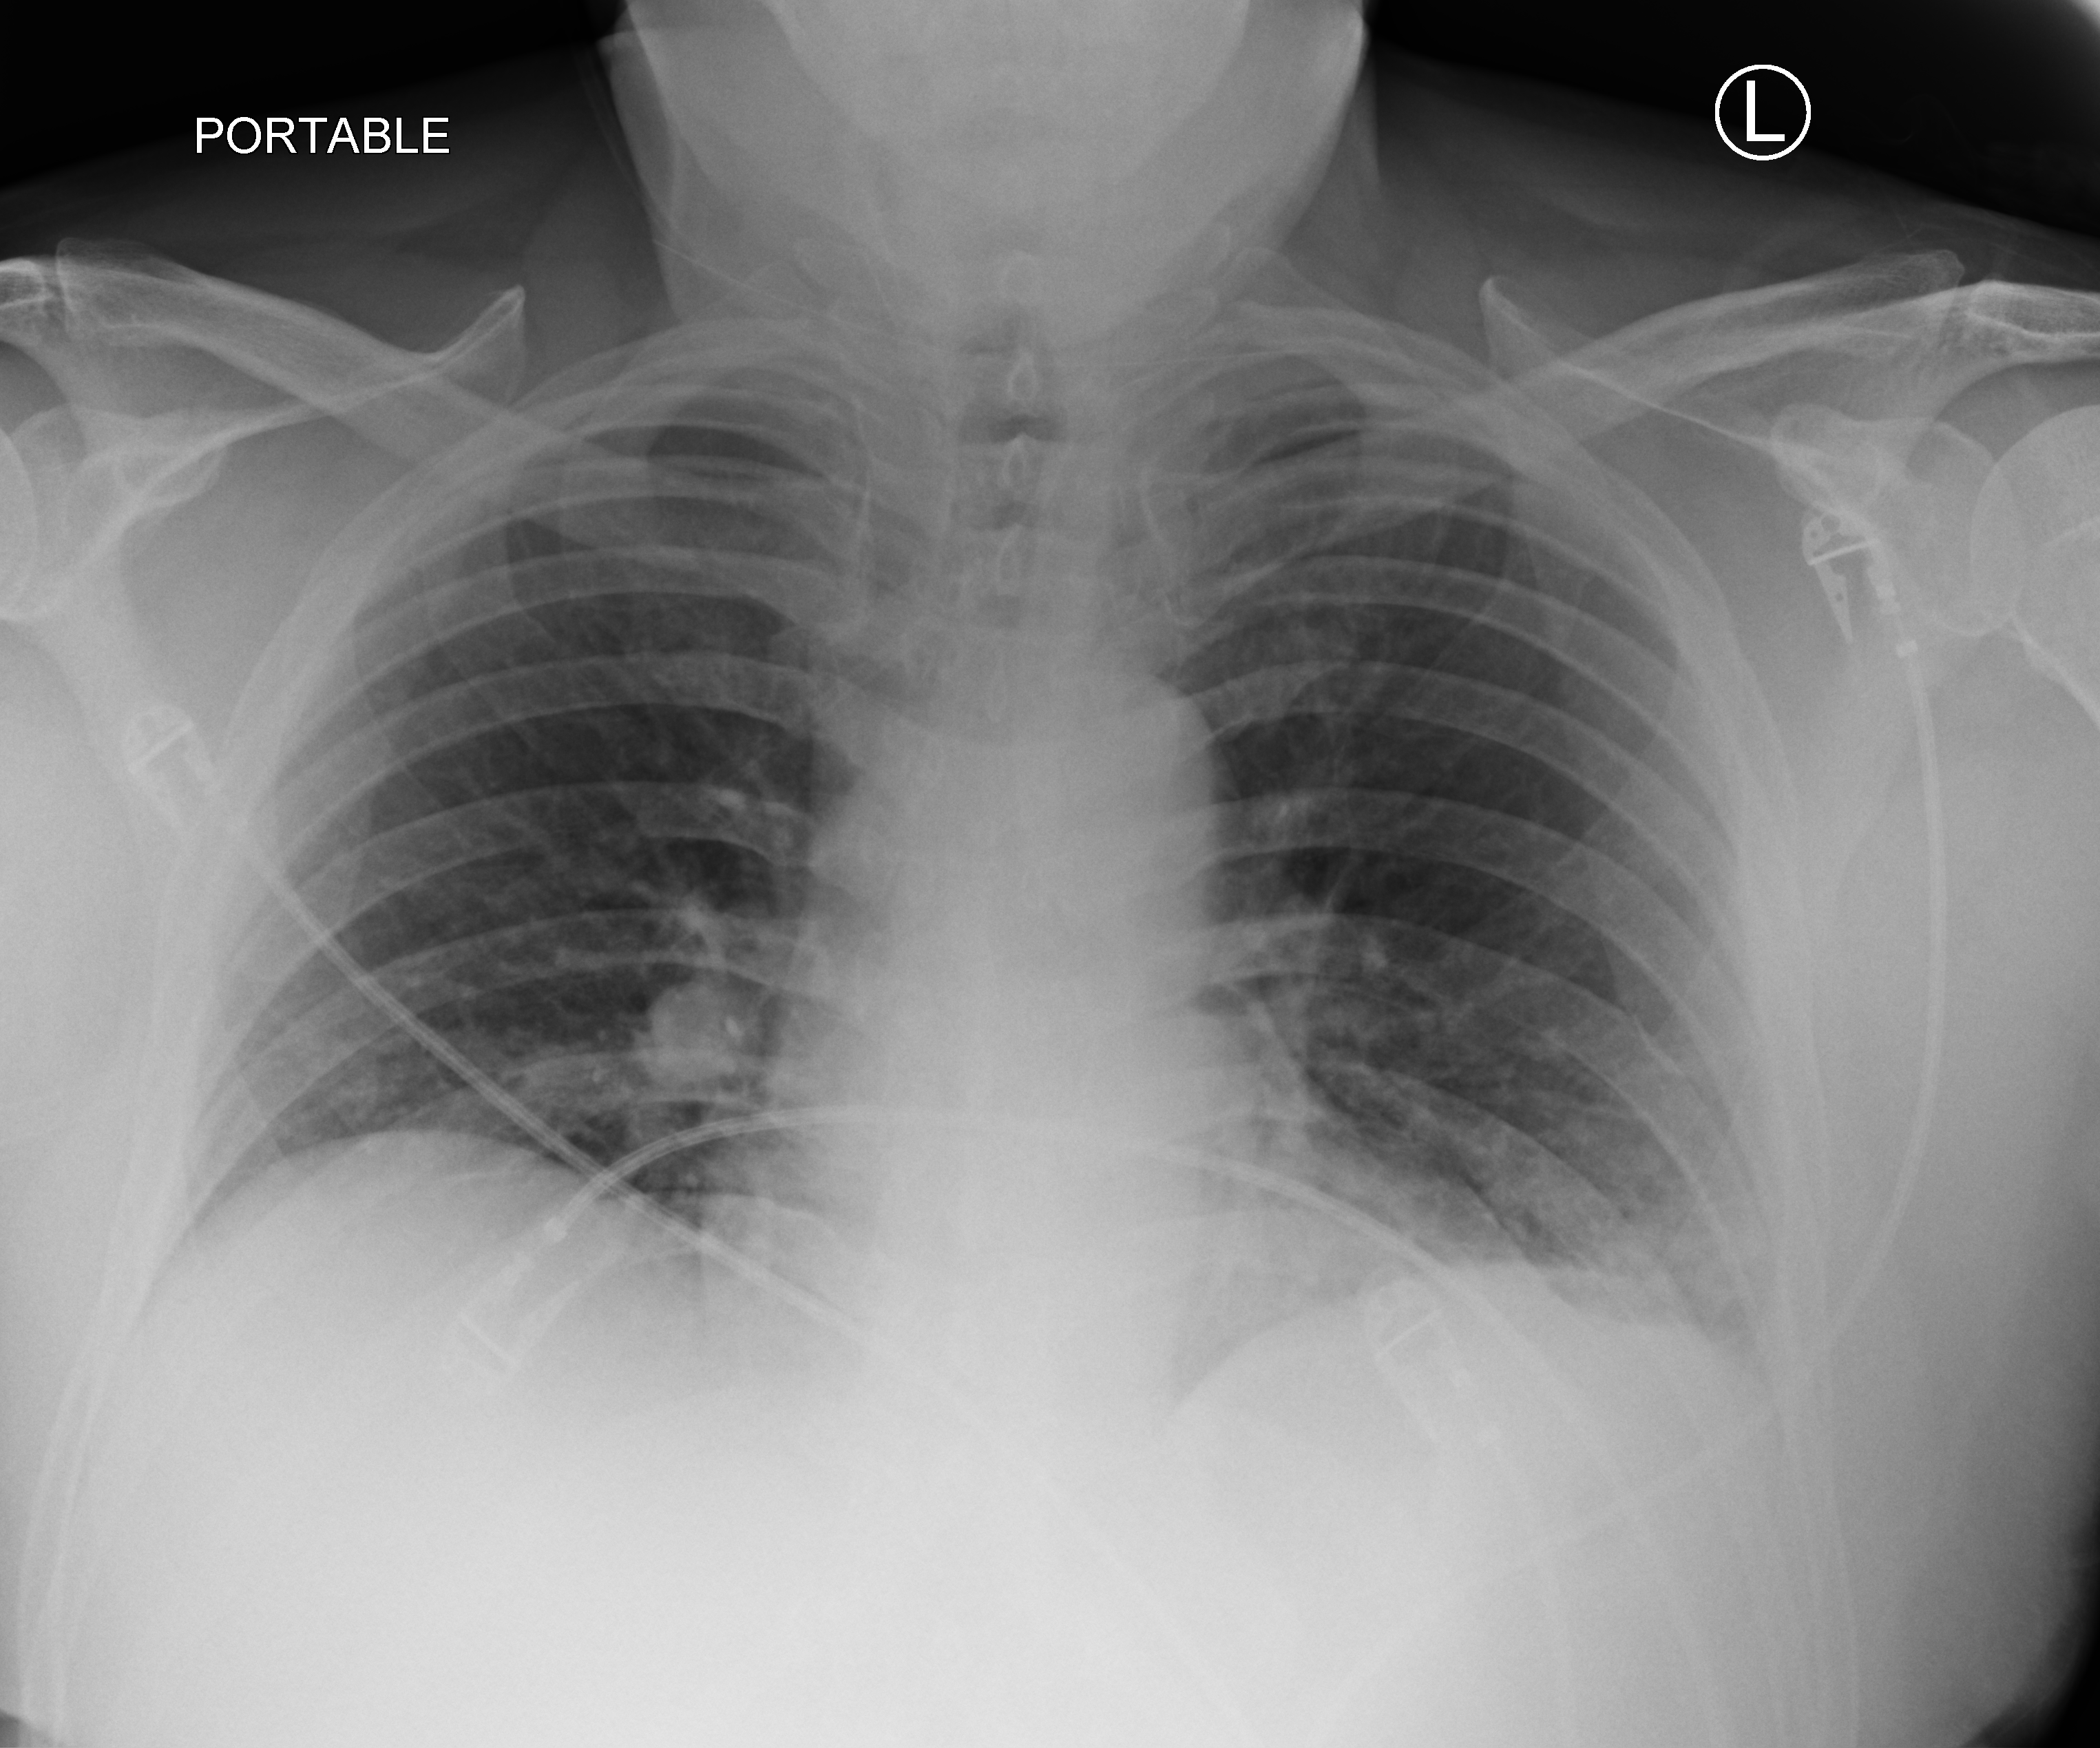
Portable chest radiograph; anteroposterior (AP) projection. Male patient hospitalised with COVID-19, age 60–74 years.
From the hospital-stay record, not from the radiograph (when in the stay this image was taken is not recorded): admitted to intensive care during this hospital stay: no; length of hospital stay: 18 days; diabetes (admission record): no.